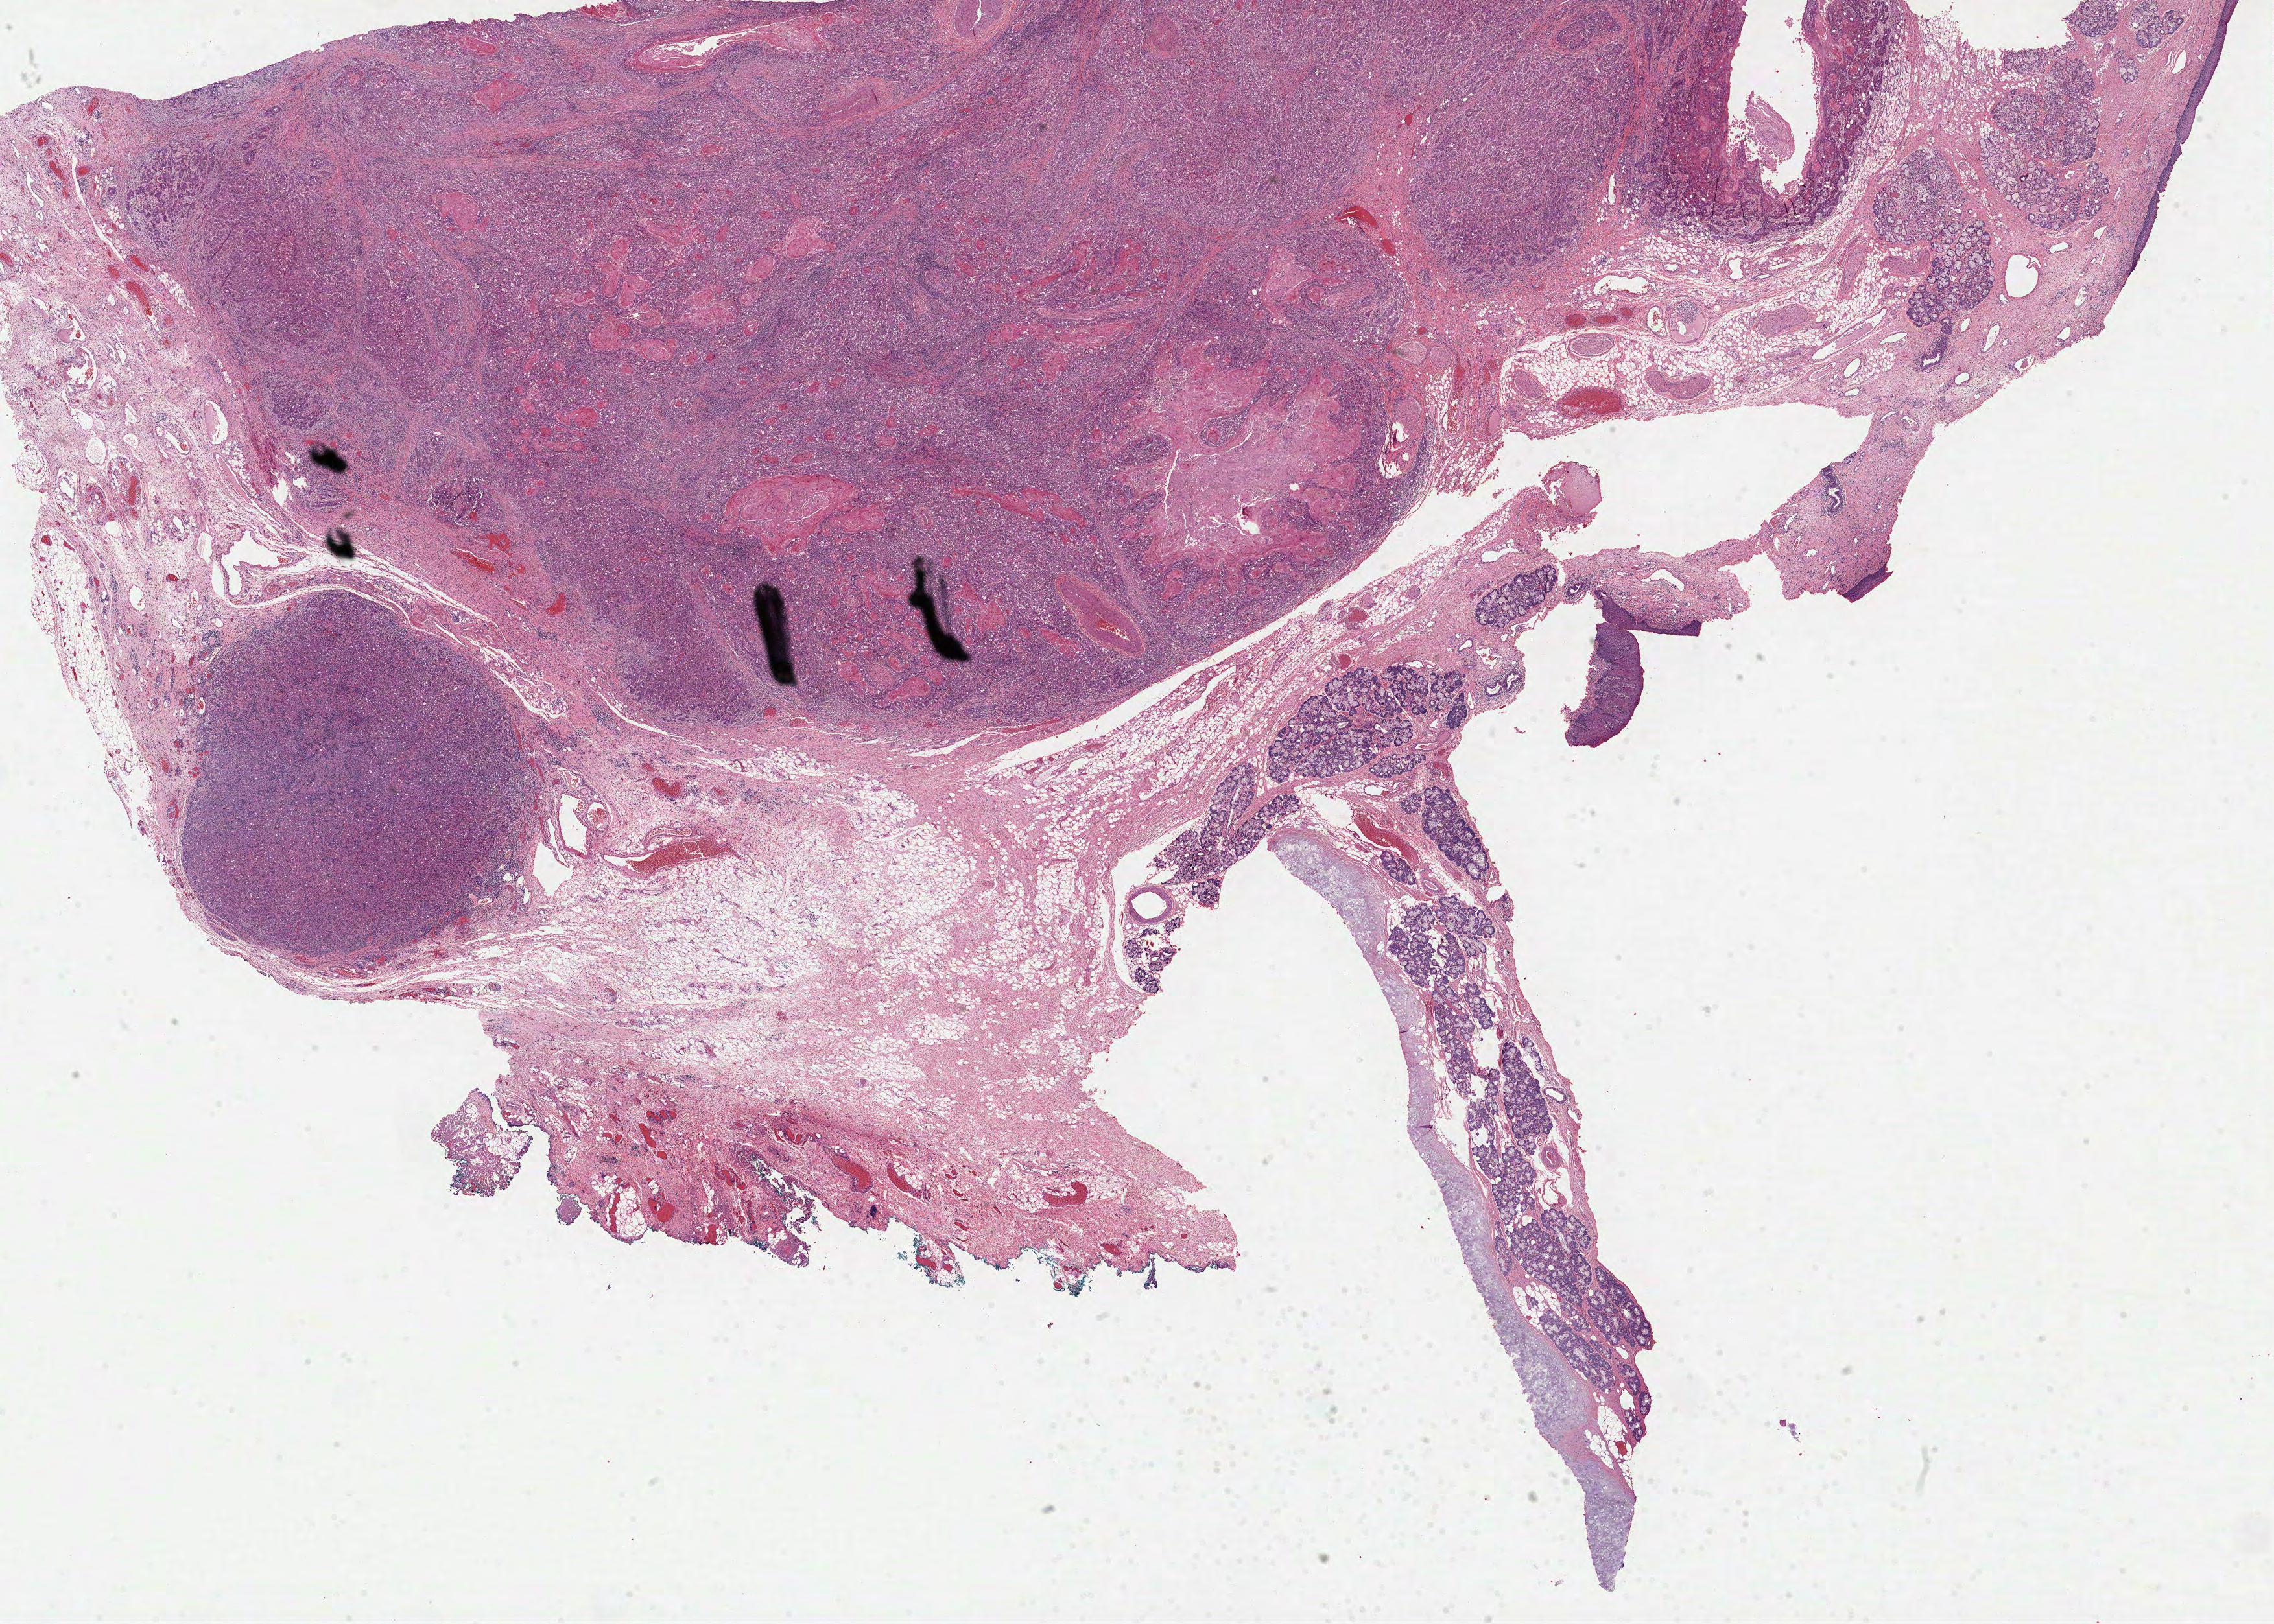
H&E-stained whole-slide image, shown as a low-resolution overview of the whole scanned area (about 28.3 x 20.2 mm), FFPE section, sample: primary tumour, head and neck. Male, age 51 years at initial diagnosis.
Diagnosis: Squamous cell carcinoma, NOS (larynx, NOS).